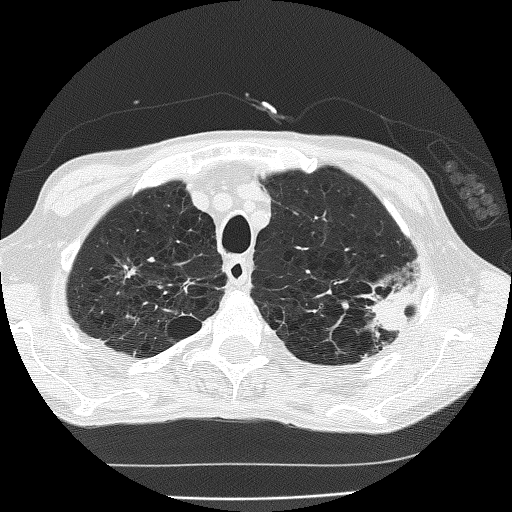
Low-dose screening chest CT, one axial slice. Position 153 of 185 along the scan axis. Reconstruction kernel FC51. 120 kVp. Lung window (W 1500 / L -600 HU). 2 mm slice thickness. 512 × 512 image matrix, field of view 320 × 320 mm.
Annotated regions visible in this slice (outlined manually by an expert reader):
- lesion 1 (tumor, upper lobe of left lung): bounding box [x1, y1, x2, y2] px = [369, 282, 418, 333]